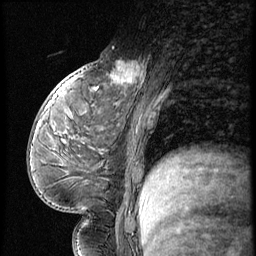
Breast MRI (dynamic contrast-enhanced), one sagittal slice. Slice 27 of 56 in the series (ordered by position). 3 images stored at this slice position (order not interpretable as contrast timing). 1.5 T. TE 4.2 ms, TR 9 ms. 256 × 256 image matrix, field of view 180 × 180 mm. Female patient, age 54 years. Case-level facts recorded for this patient, not image findings: setting: breast cancer imaged before/during neoadjuvant chemotherapy; receptor status: triple-negative.
Outlined on this slice (semi-automatic segmentation, software-assisted and operator-edited):
- analysis volume of interest (the breast-tissue region the enhancement analysis was run in; not a lesion): bounding box [x1, y1, x2, y2] px = [99, 53, 149, 102]
- tumour enhancement mask (voxels above the 140 % enhancement threshold inside the analysis volume of interest): [111, 61, 145, 90]